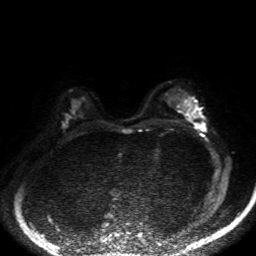
Breast MRI, one axial slice. Position 32 of 50 along the scan axis. Diffusion-weighted series; image 2 of 4 stored at this slice position (different b-values; order by instance number). 1.5 T. 4 mm slice thickness. 256 × 256 image matrix, field of view 320 × 320 mm. Female patient.
Annotated regions visible in this slice (outlined manually by an expert reader):
- tumour on diffusion-weighted imaging: box from (x=195, y=123) to (x=205, y=128) px